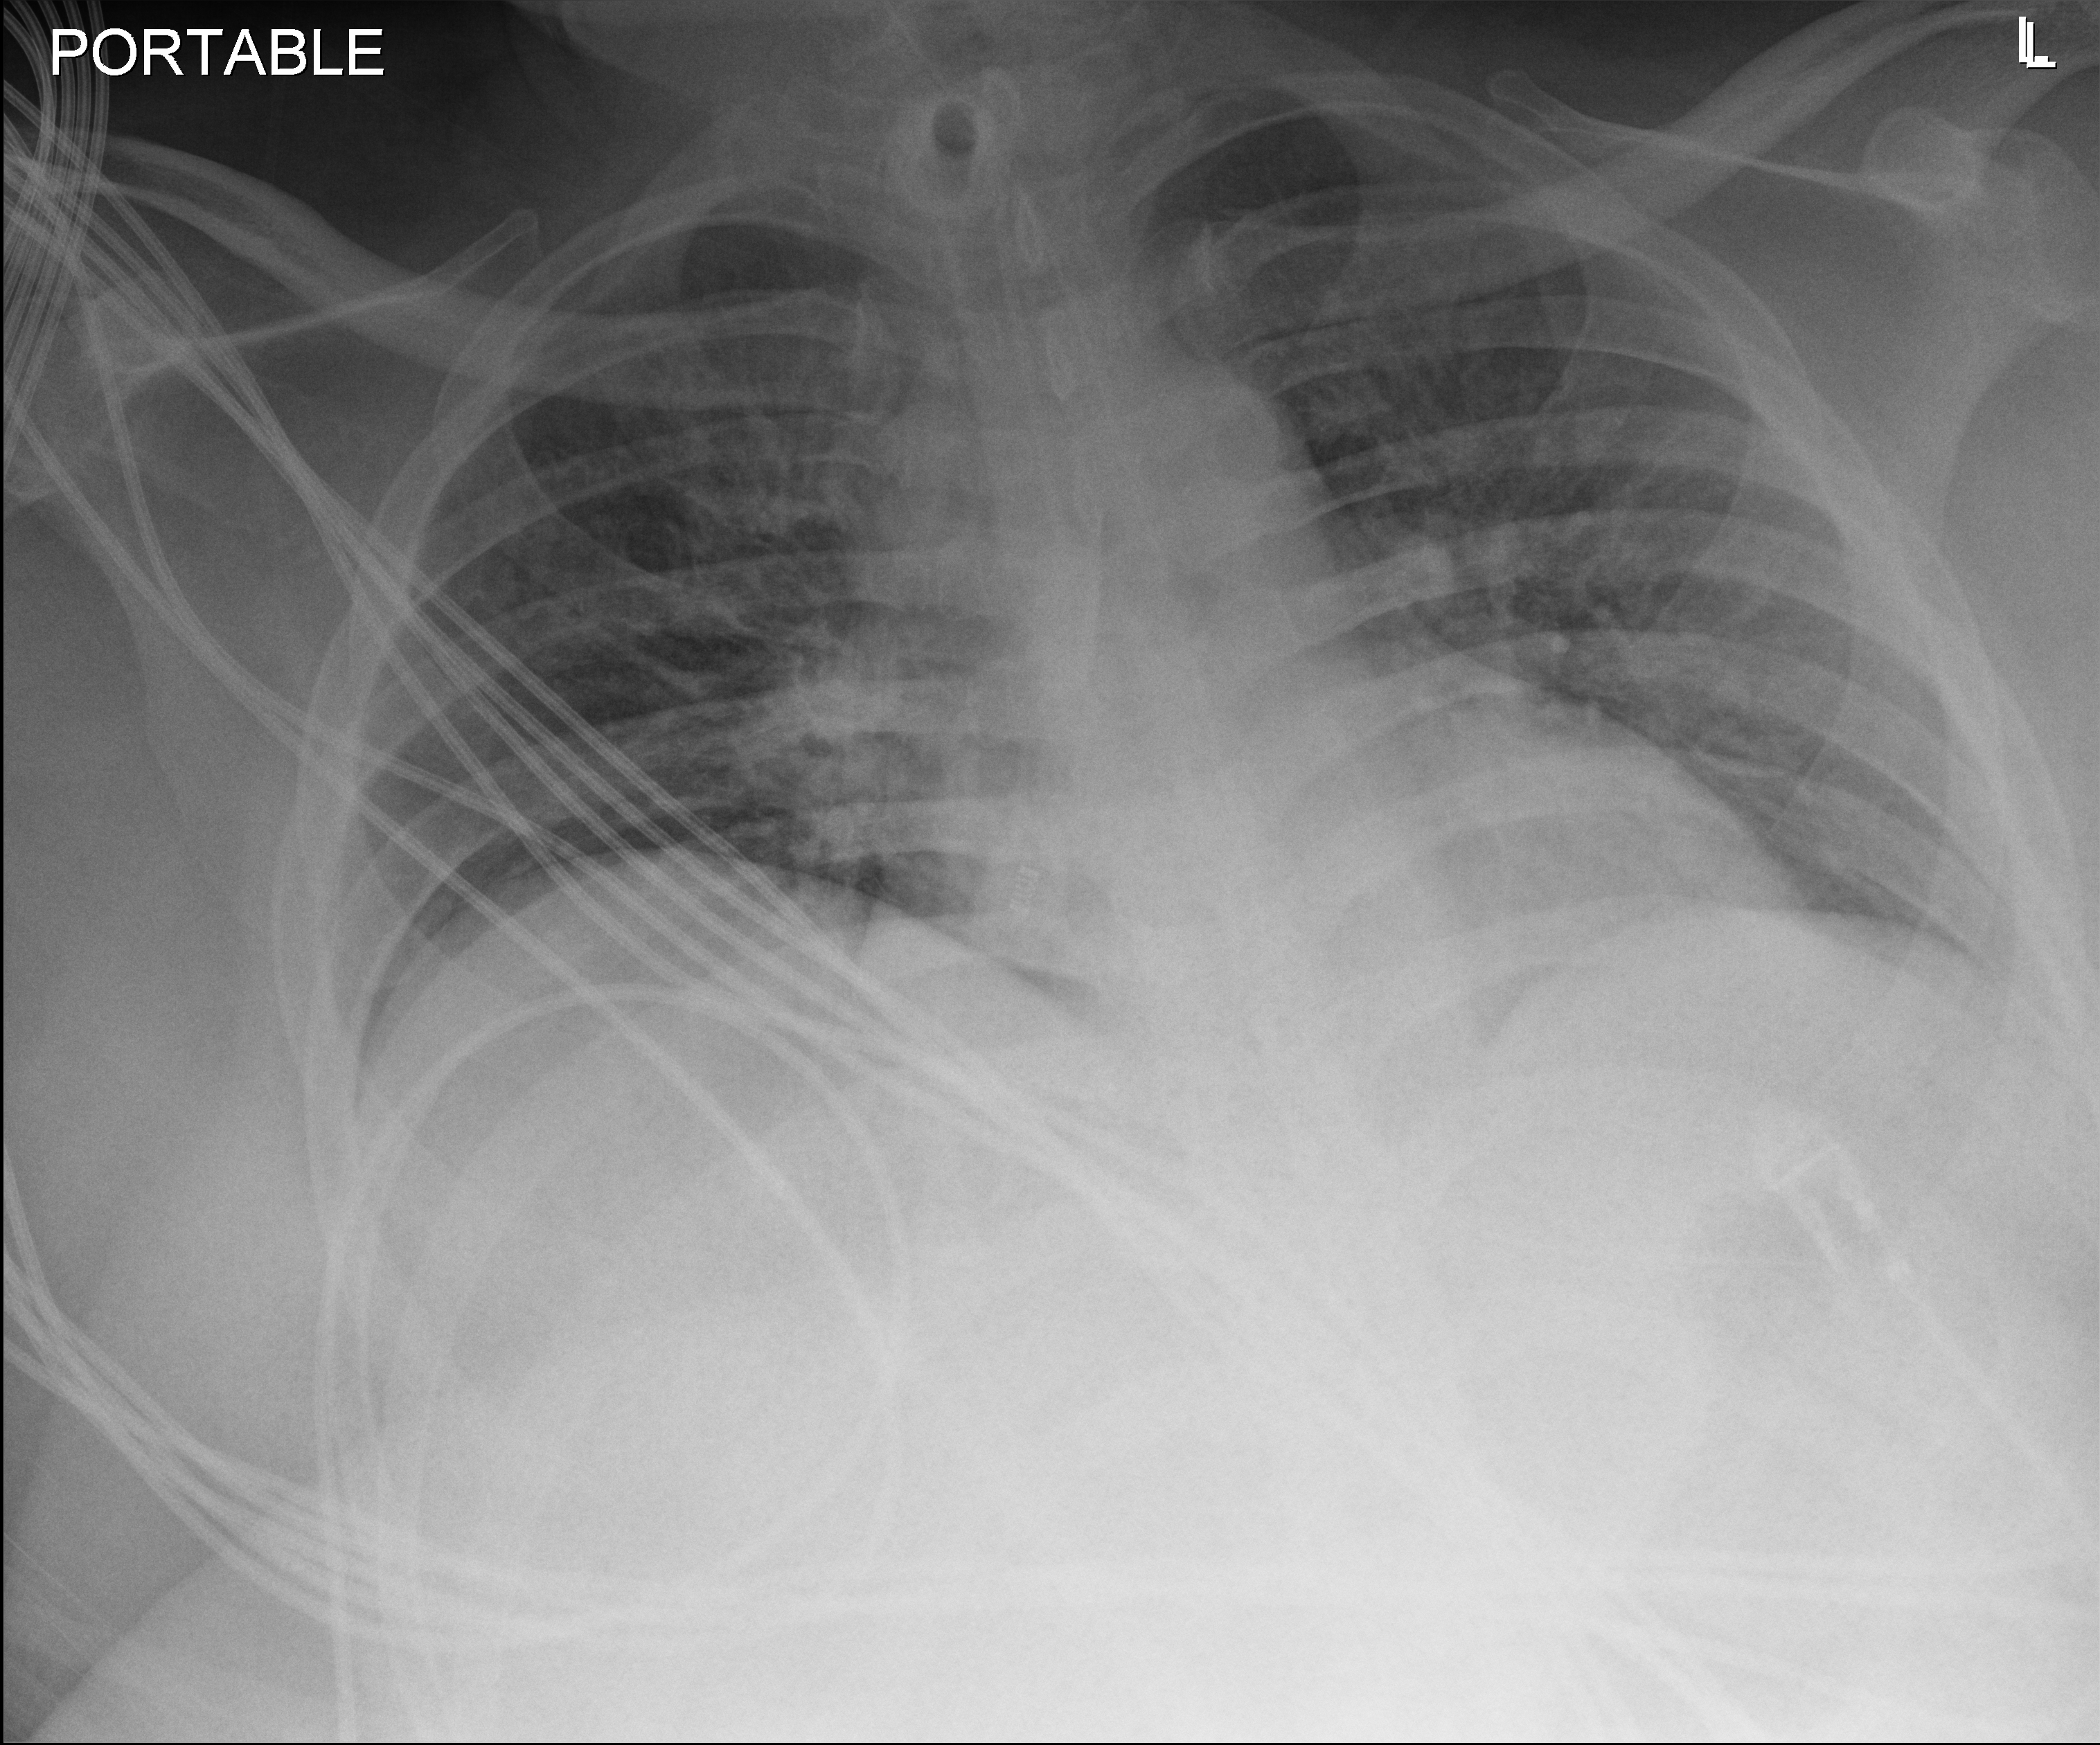
Chest X-ray (portable), anteroposterior (AP) projection. Patient hospitalised with COVID-19; male, aged 18–59 years.
Hospital-stay facts (about this admission, not read from this image; timing relative to this image not recorded):
- length of hospital stay: 69 days
- other chronic lung disease (admission record): yes